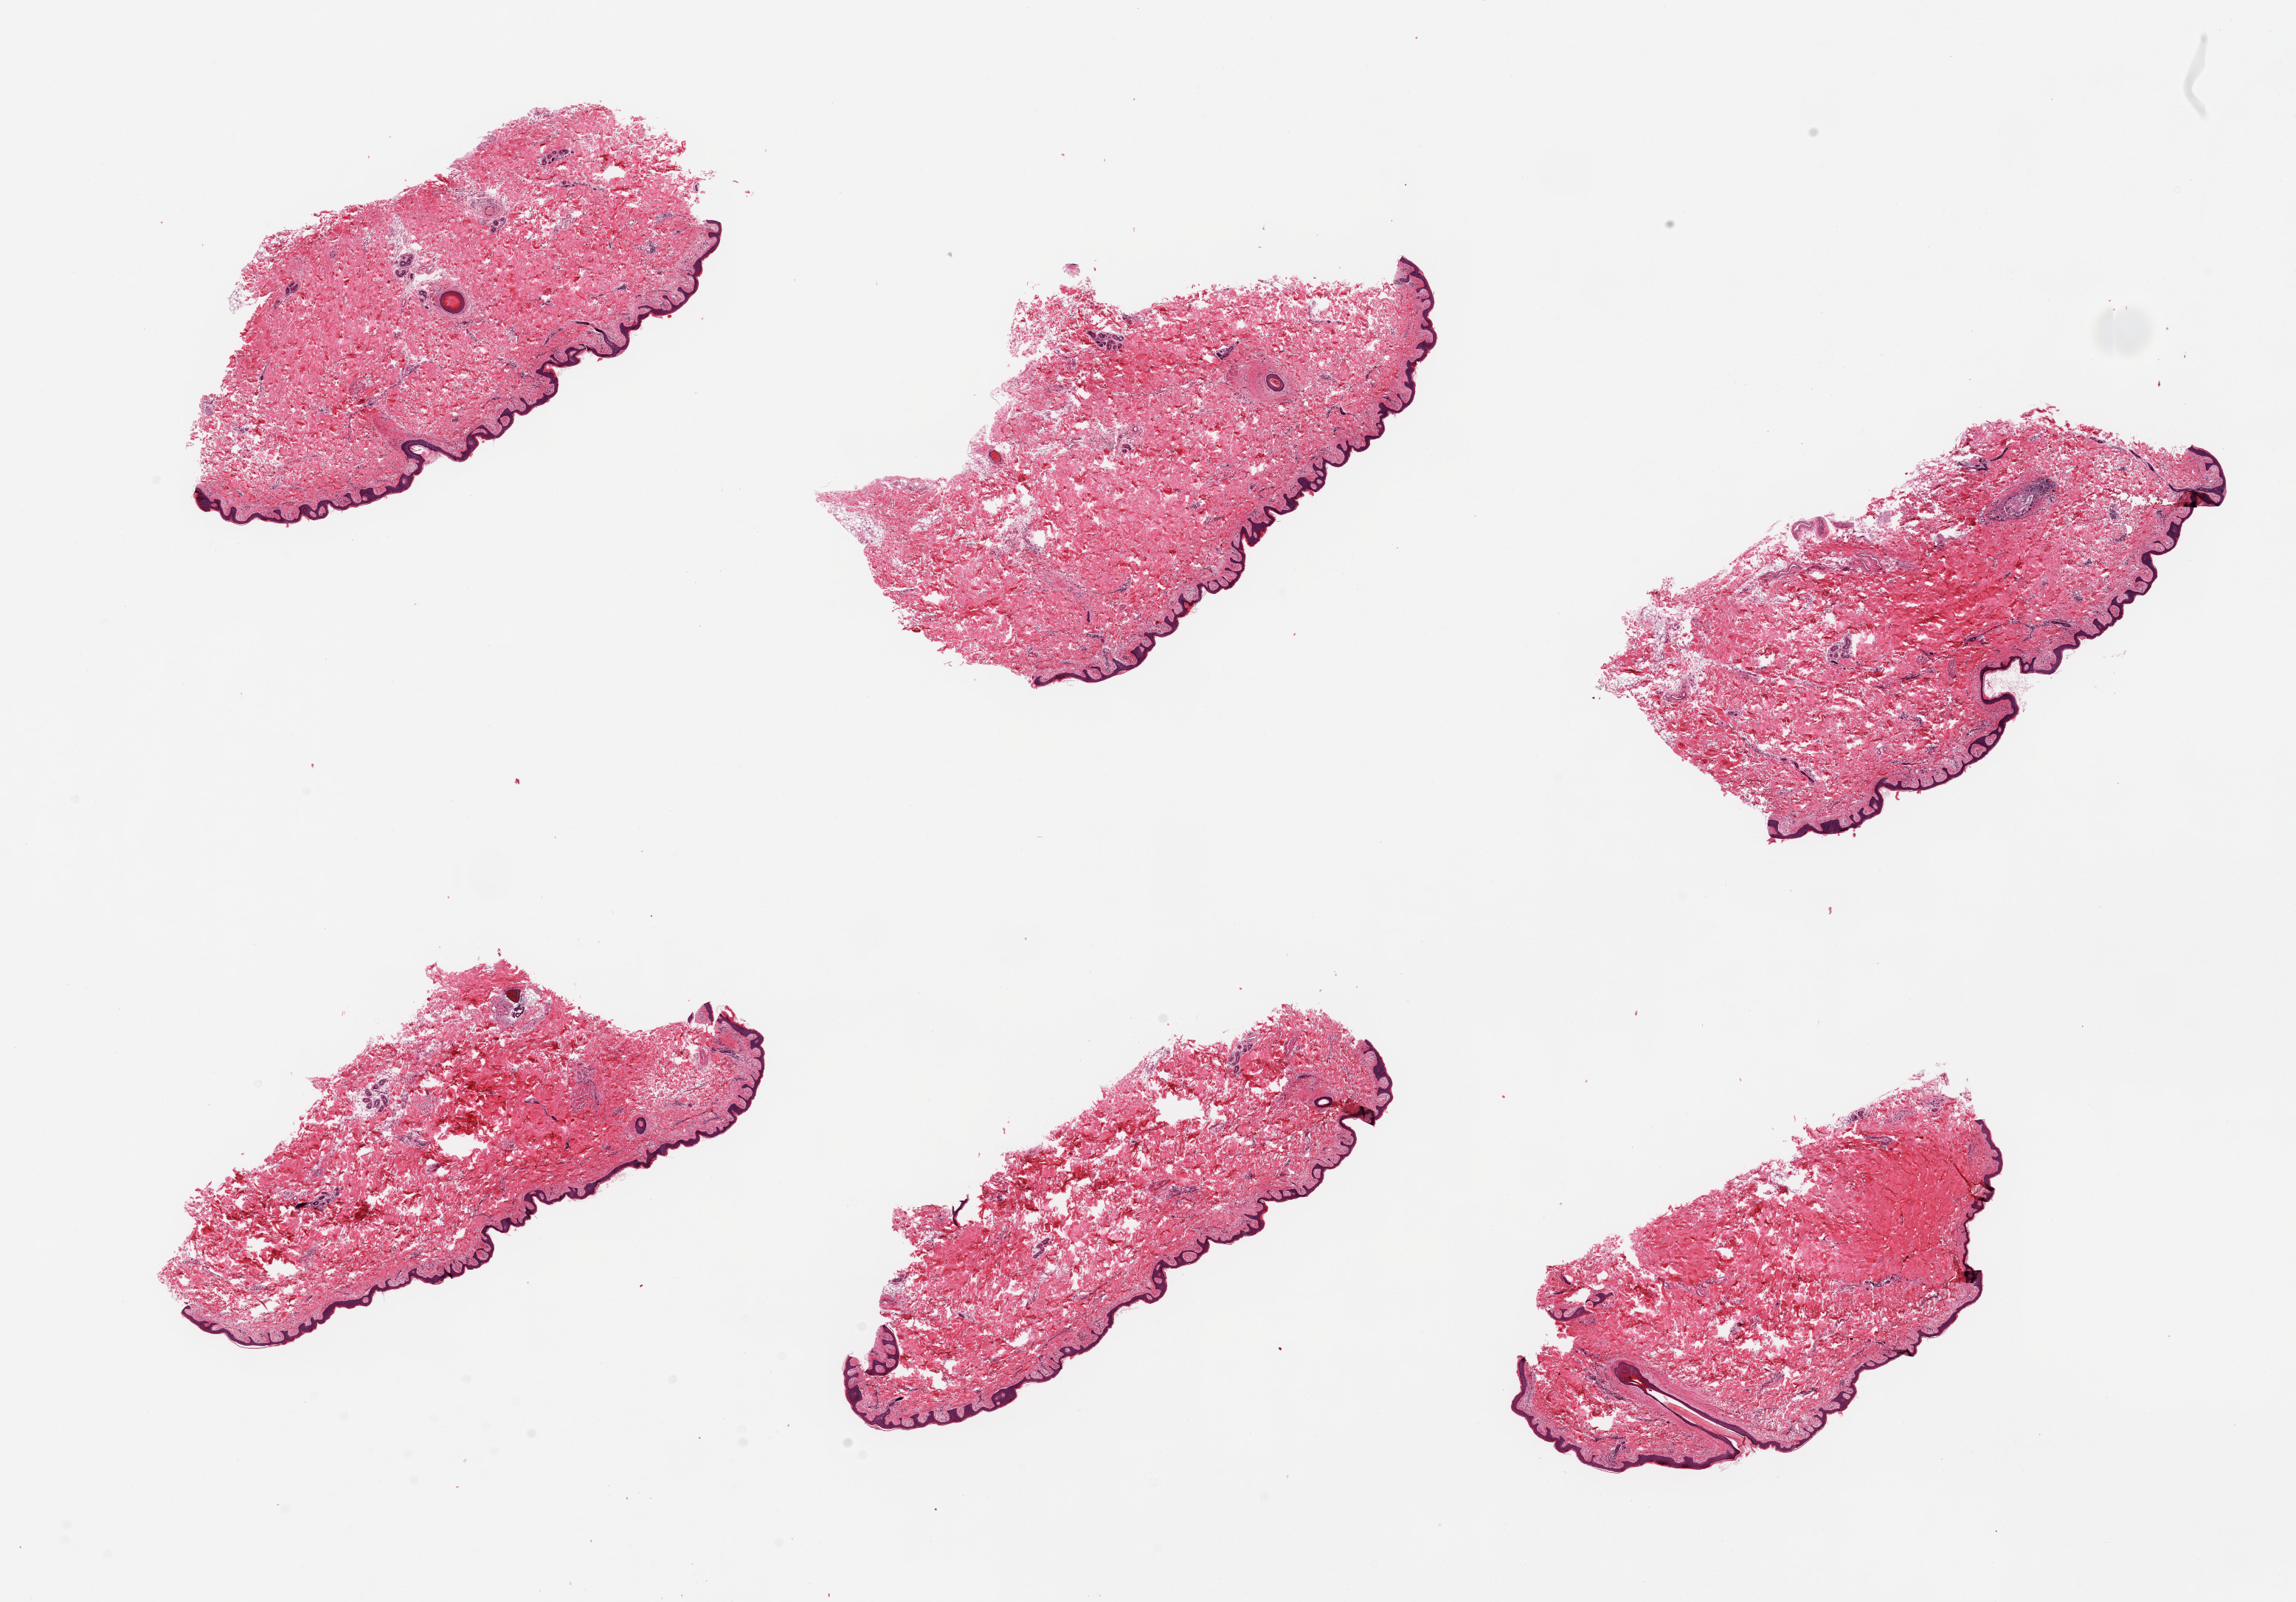
Hematoxylin and eosin (H&E) whole-slide image, whole scanned area (about 24.6 x 17.2 mm, slide scanned at 20x) shown as a low-resolution overview. PAXgene-fixed paraffin-embedded (PFPE) section. Target tissue: skin of suprapubic region. Donor tissue sample. Donor sex: male.
Reviewer comment on this tissue sample: 6 pieces; 1 has focal foreign body reaction, 0.27mm.